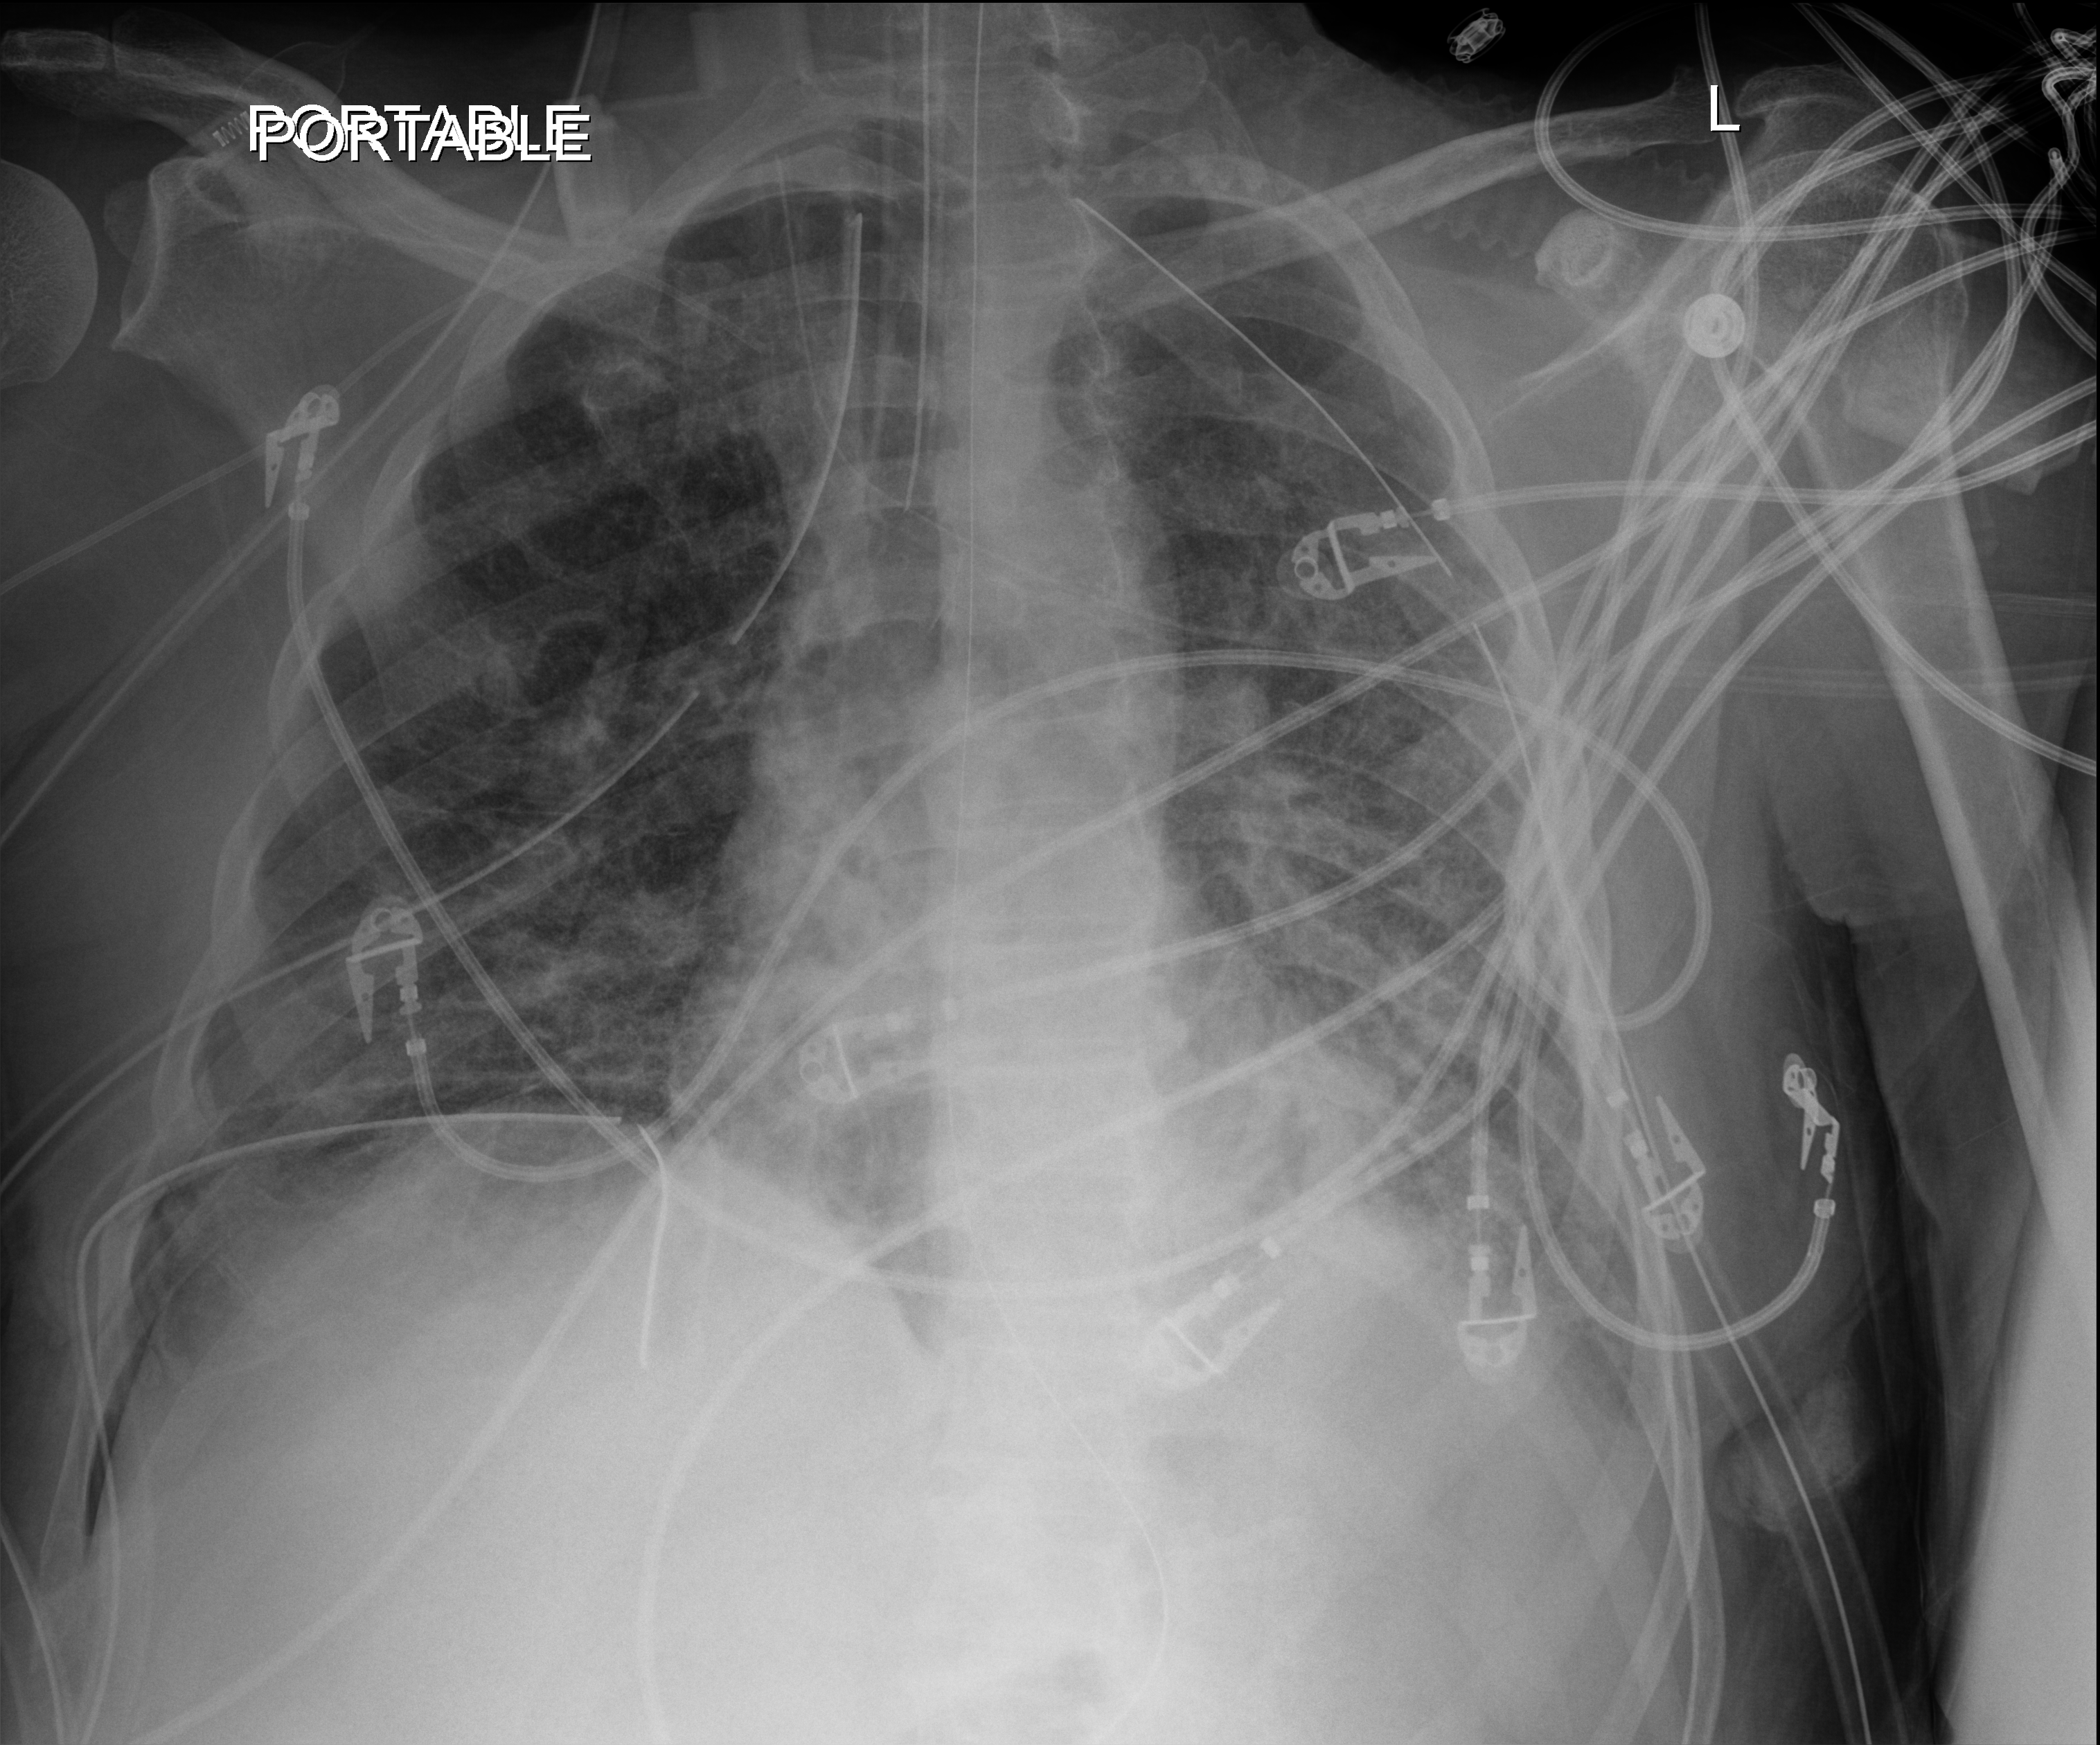
Bedside chest radiograph (digital radiography); anteroposterior (AP) projection. Patient hospitalised with COVID-19; male, aged 18–59 years.
Admission-level facts for this patient (not findings on this image; timing relative to this image not recorded): mechanically ventilated during this hospital stay: yes; admitted to intensive care during this hospital stay: yes.